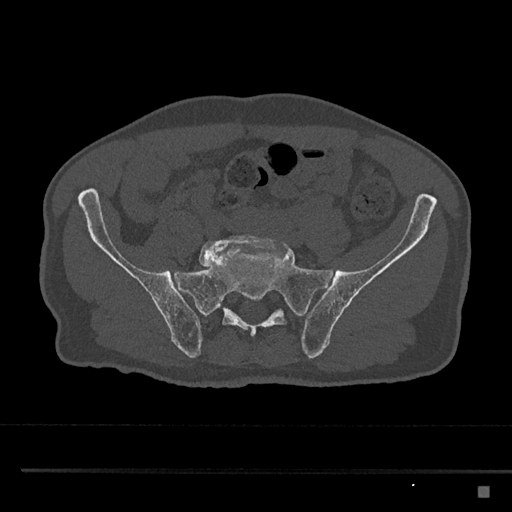
CT including the spine, one axial slice; slice 530 of 797 in the series (ordered by position); reconstruction kernel Br40s/3; 120 kVp; bone window (W 1800 / L 400 HU); 512 × 512 image matrix, field of view 391 × 391 mm. Male patient, age 59 years. From the clinical record (not read from this slice): primary cancer: prostate.
Structures marked on this image (semi-automatically segmented with operator editing):
- L5 vertebra: bounding box [x1, y1, x2, y2] px = [199, 235, 286, 268]